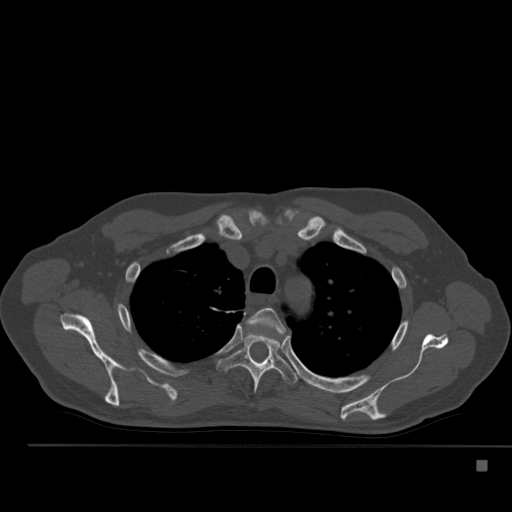
CT including the spine, one axial slice. Reconstruction kernel Br40s. 120 kVp. Bone window (W 1800 / L 400 HU). 1.5 mm slice thickness. 512 × 512 image matrix, field of view 408 × 408 mm. Male patient, age 70 years. Case-level facts recorded for this patient, not image findings: primary cancer: renal; vertebrae with lytic lesions (as recorded): T4, T6, T10, T12, L3, L4, L5.
Outlined on this slice (semi-automatic segmentation, software-assisted and operator-edited):
- T3 vertebra: bounding box (x1, y1, x2, y2) in pixels: (246, 308, 286, 334)
- T4 vertebra: (217, 329, 298, 394)